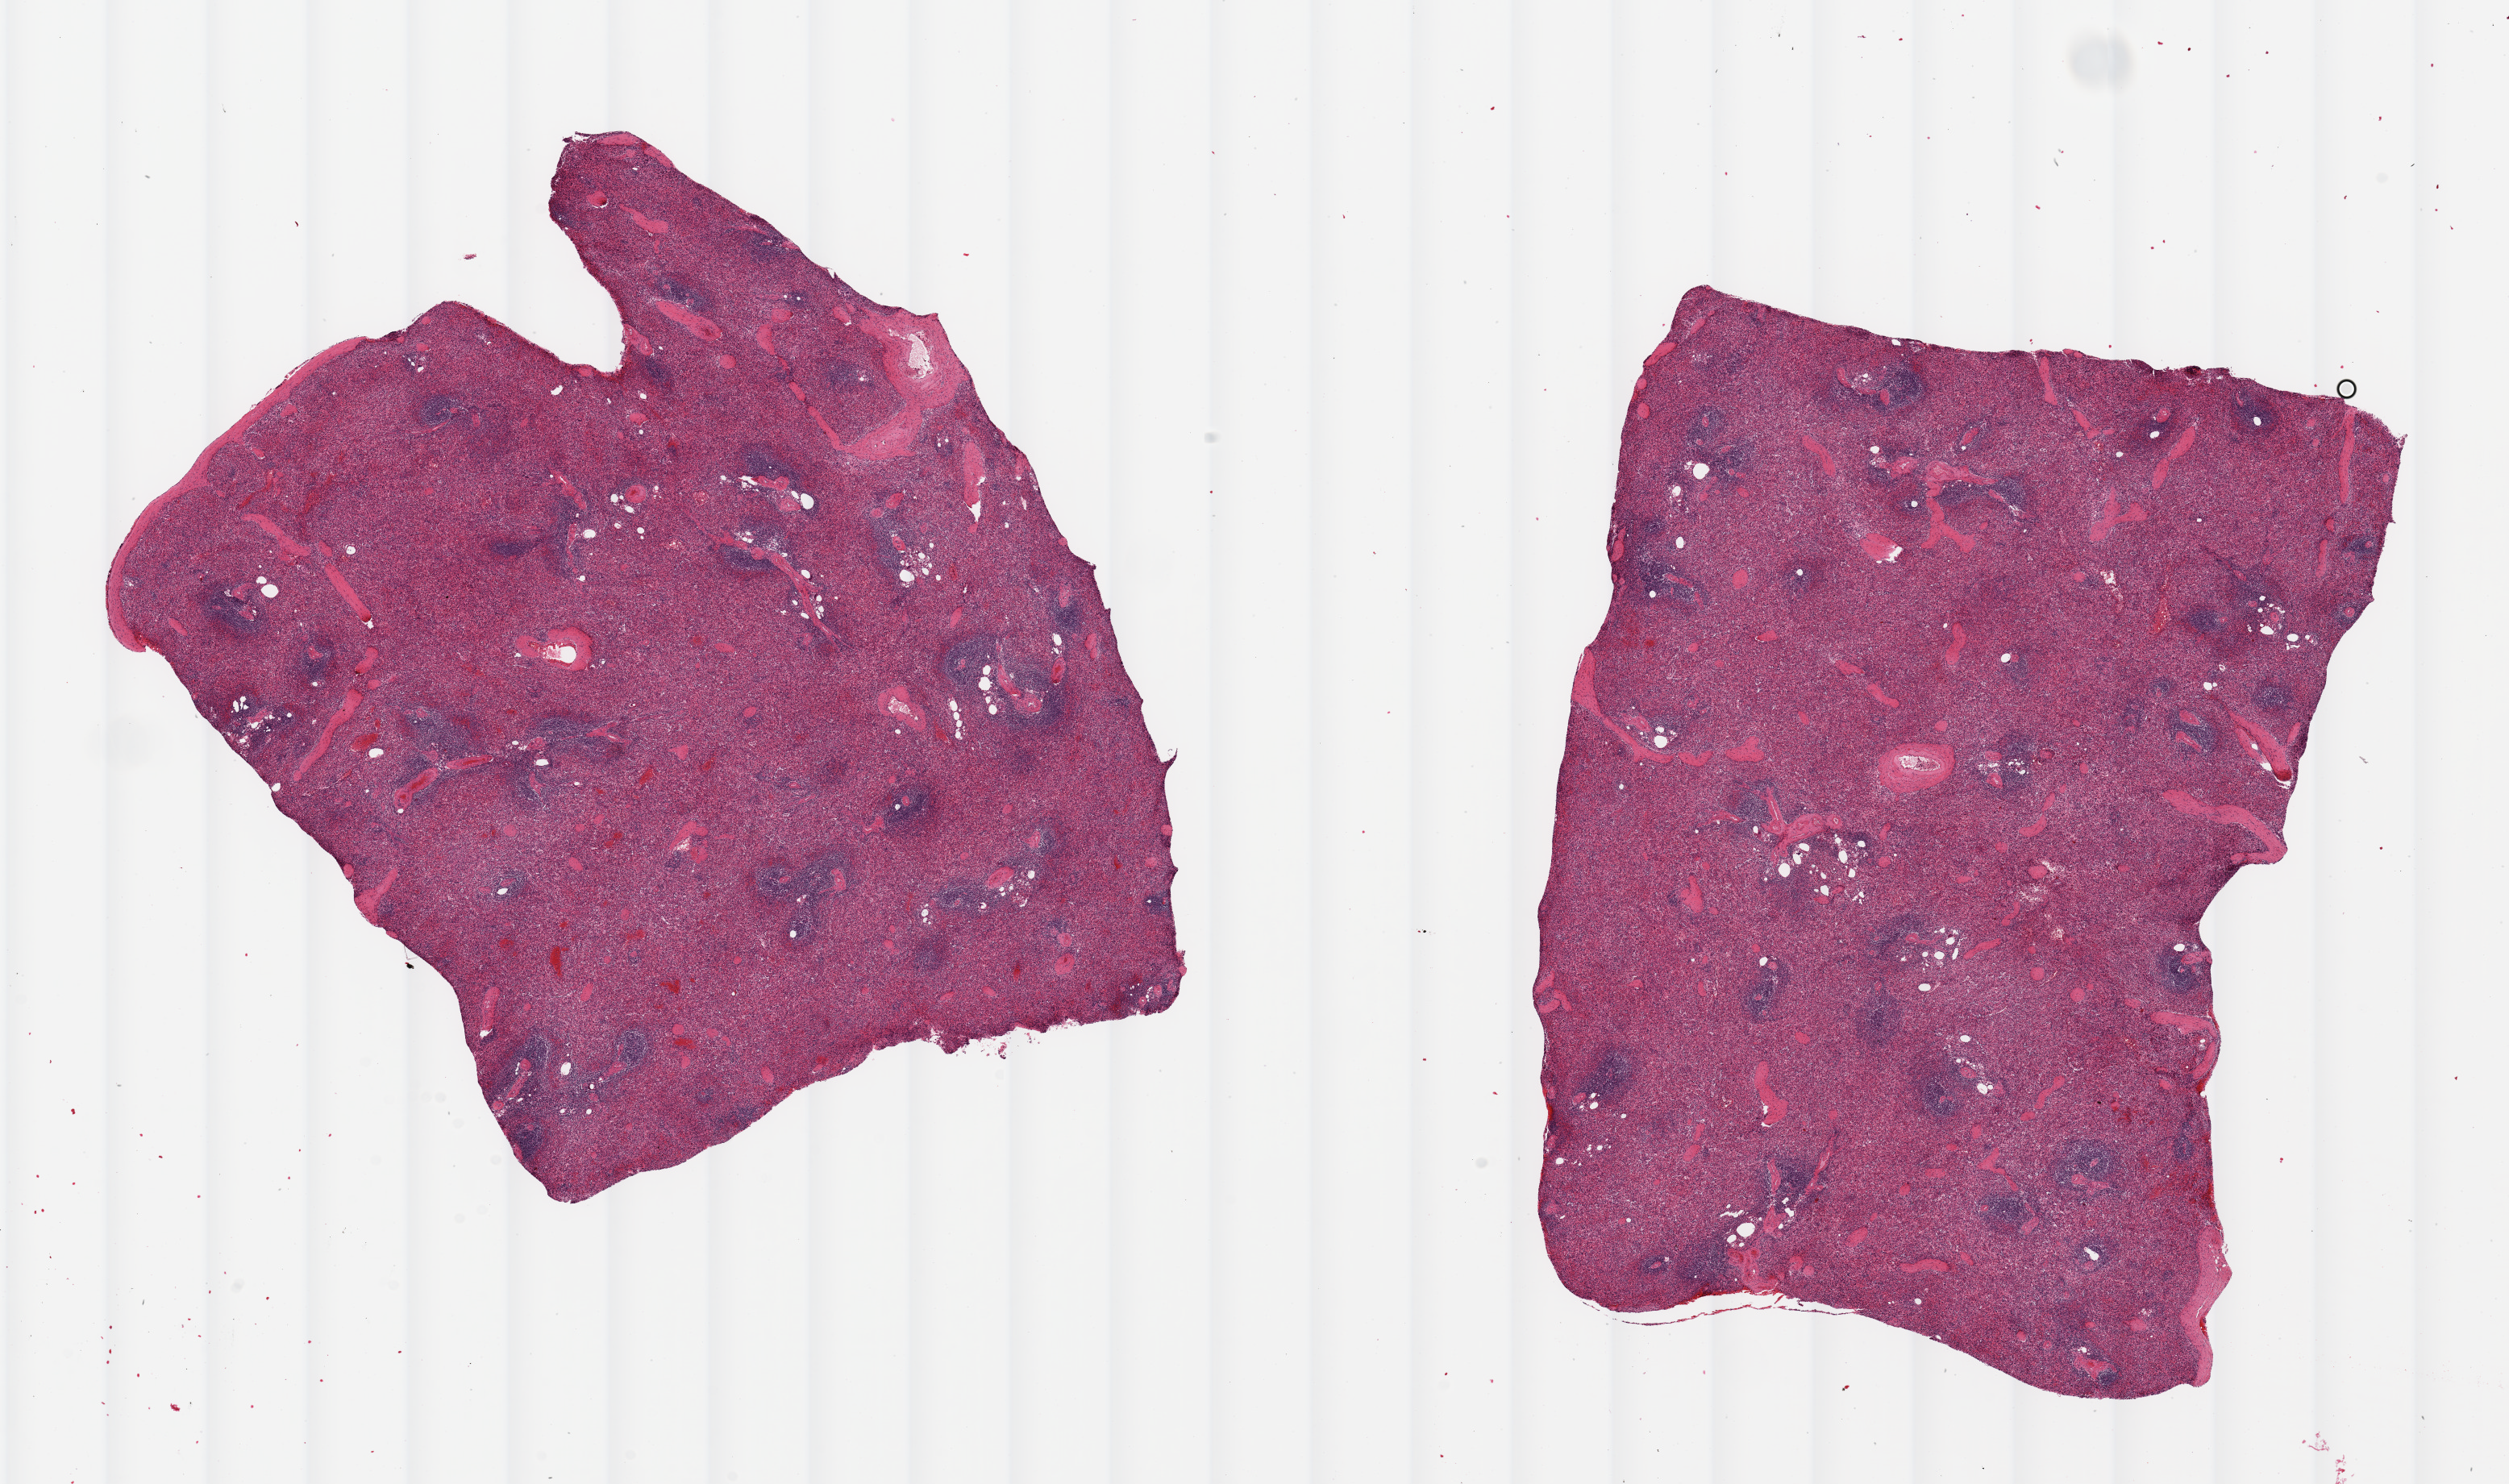
Haematoxylin and eosin whole-slide image, brightfield, whole scanned area (about 24.6 x 14.6 mm) shown as a low-resolution overview. PAXgene-fixed paraffin-embedded (PFPE) section. Section of spleen (target tissue). Donor tissue sample. Donor: male.
Review note (as recorded): 2 pieces ~10x7mm. Moderate congestion.